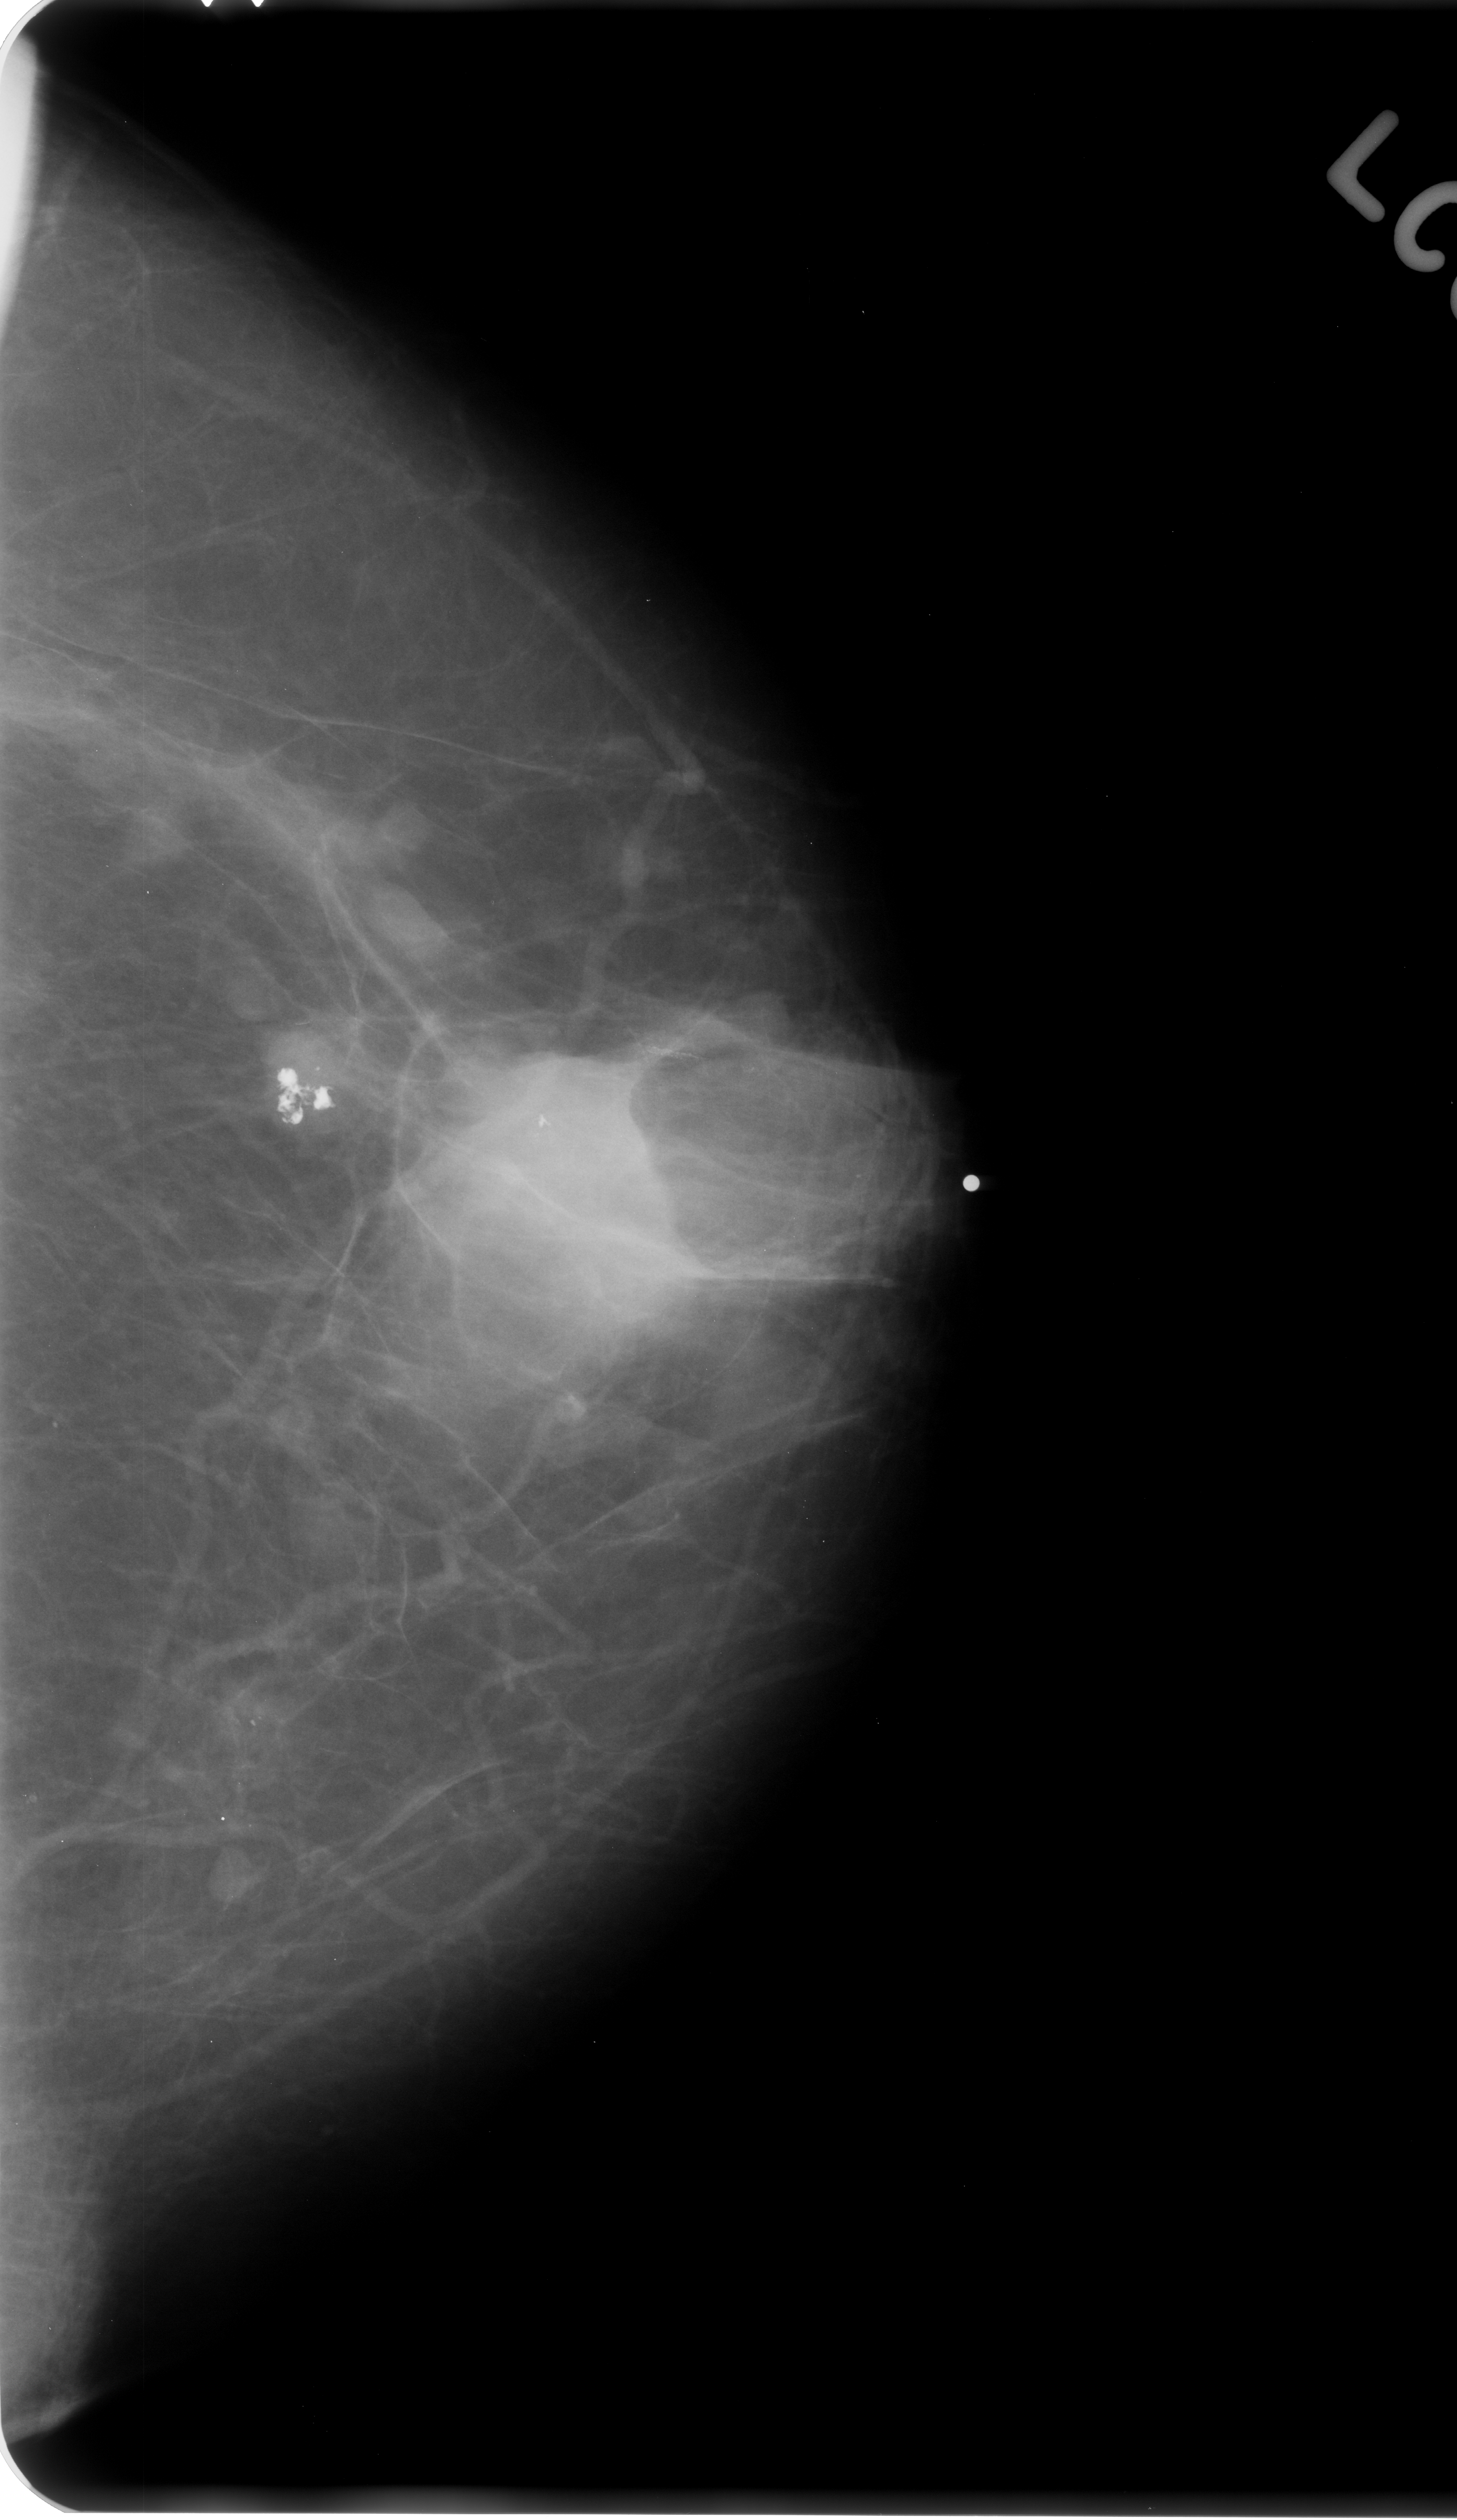
Scanned film-screen mammogram; left breast; craniocaudal (CC) view; BI-RADS breast density category 2 (scale 1–4).
Mass, shape irregular, margins ill defined; BI-RADS assessment category 4; pathology result (as recorded, not read from the image): malignant.